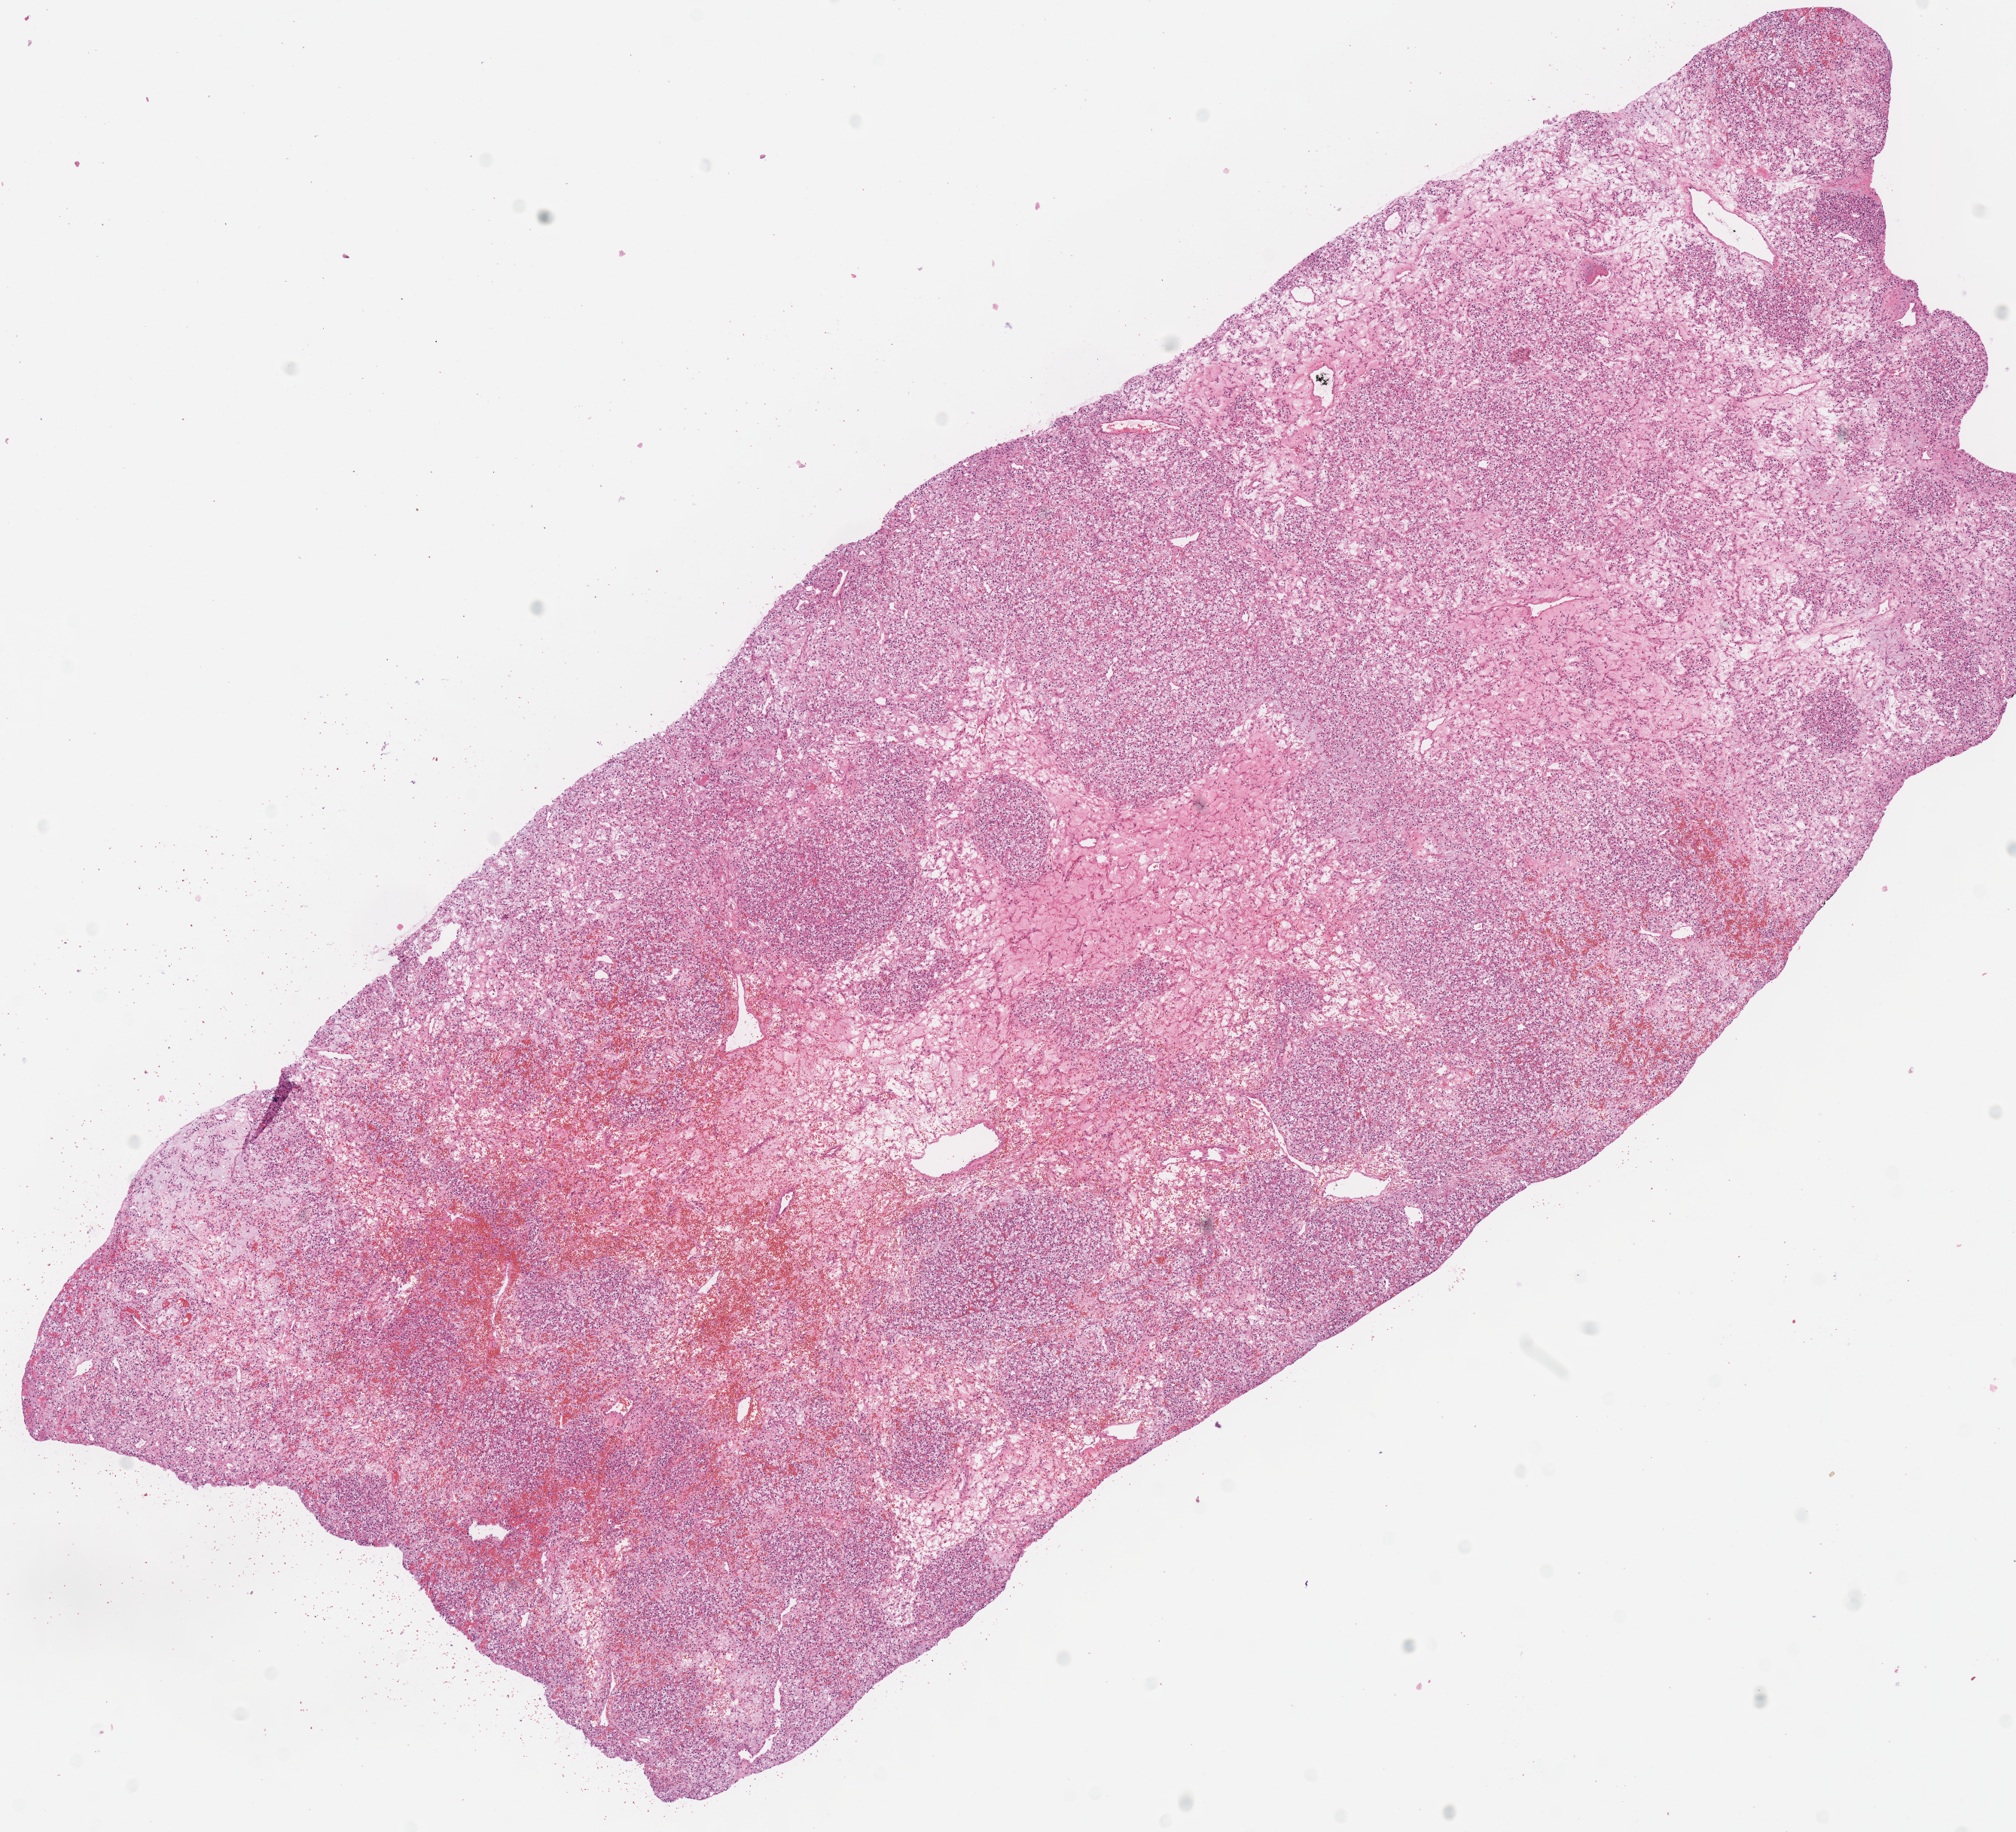
Digitized Hematoxylin and eosin (H&E) stained tissue section (whole slide), low-resolution overview of the scanned area, about 10.5 x 9.6 mm (slide scanned at 40x); FFPE section; sample: primary tumour, kidney. Male, age 52 years at initial diagnosis. Histologic grade: G2 (moderately differentiated).
Histologic diagnosis: Clear cell adenocarcinoma, NOS. AJCC pathologic stage: I.